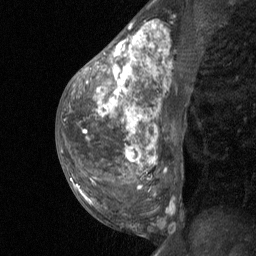
Breast MRI (dynamic contrast-enhanced), one sagittal slice; slice 33 of 64 in the series (ordered by position); dynamic contrast-enhanced study with each time point stored as its own series, time point 2 of 3 at this slice position (early post-contrast, ordered by acquisition time); 1.5 T; TE 4.8 ms, TR 27 ms; 256 × 256 image matrix, field of view 180 × 180 mm. Female patient, age 36 years. Case-level facts recorded for this patient, not image findings: setting: breast cancer imaged before/during neoadjuvant chemotherapy; receptor status: HR-positive, HER2-negative.
Structures marked on this image (semi-automatically segmented with operator editing):
- analysis volume of interest (the breast-tissue region the enhancement analysis was run in; not a lesion): bounding box [x1, y1, x2, y2] px = [67, 12, 187, 238]
- tumour enhancement mask (voxels above the 90 % enhancement threshold inside the analysis volume of interest): [84, 24, 149, 166]